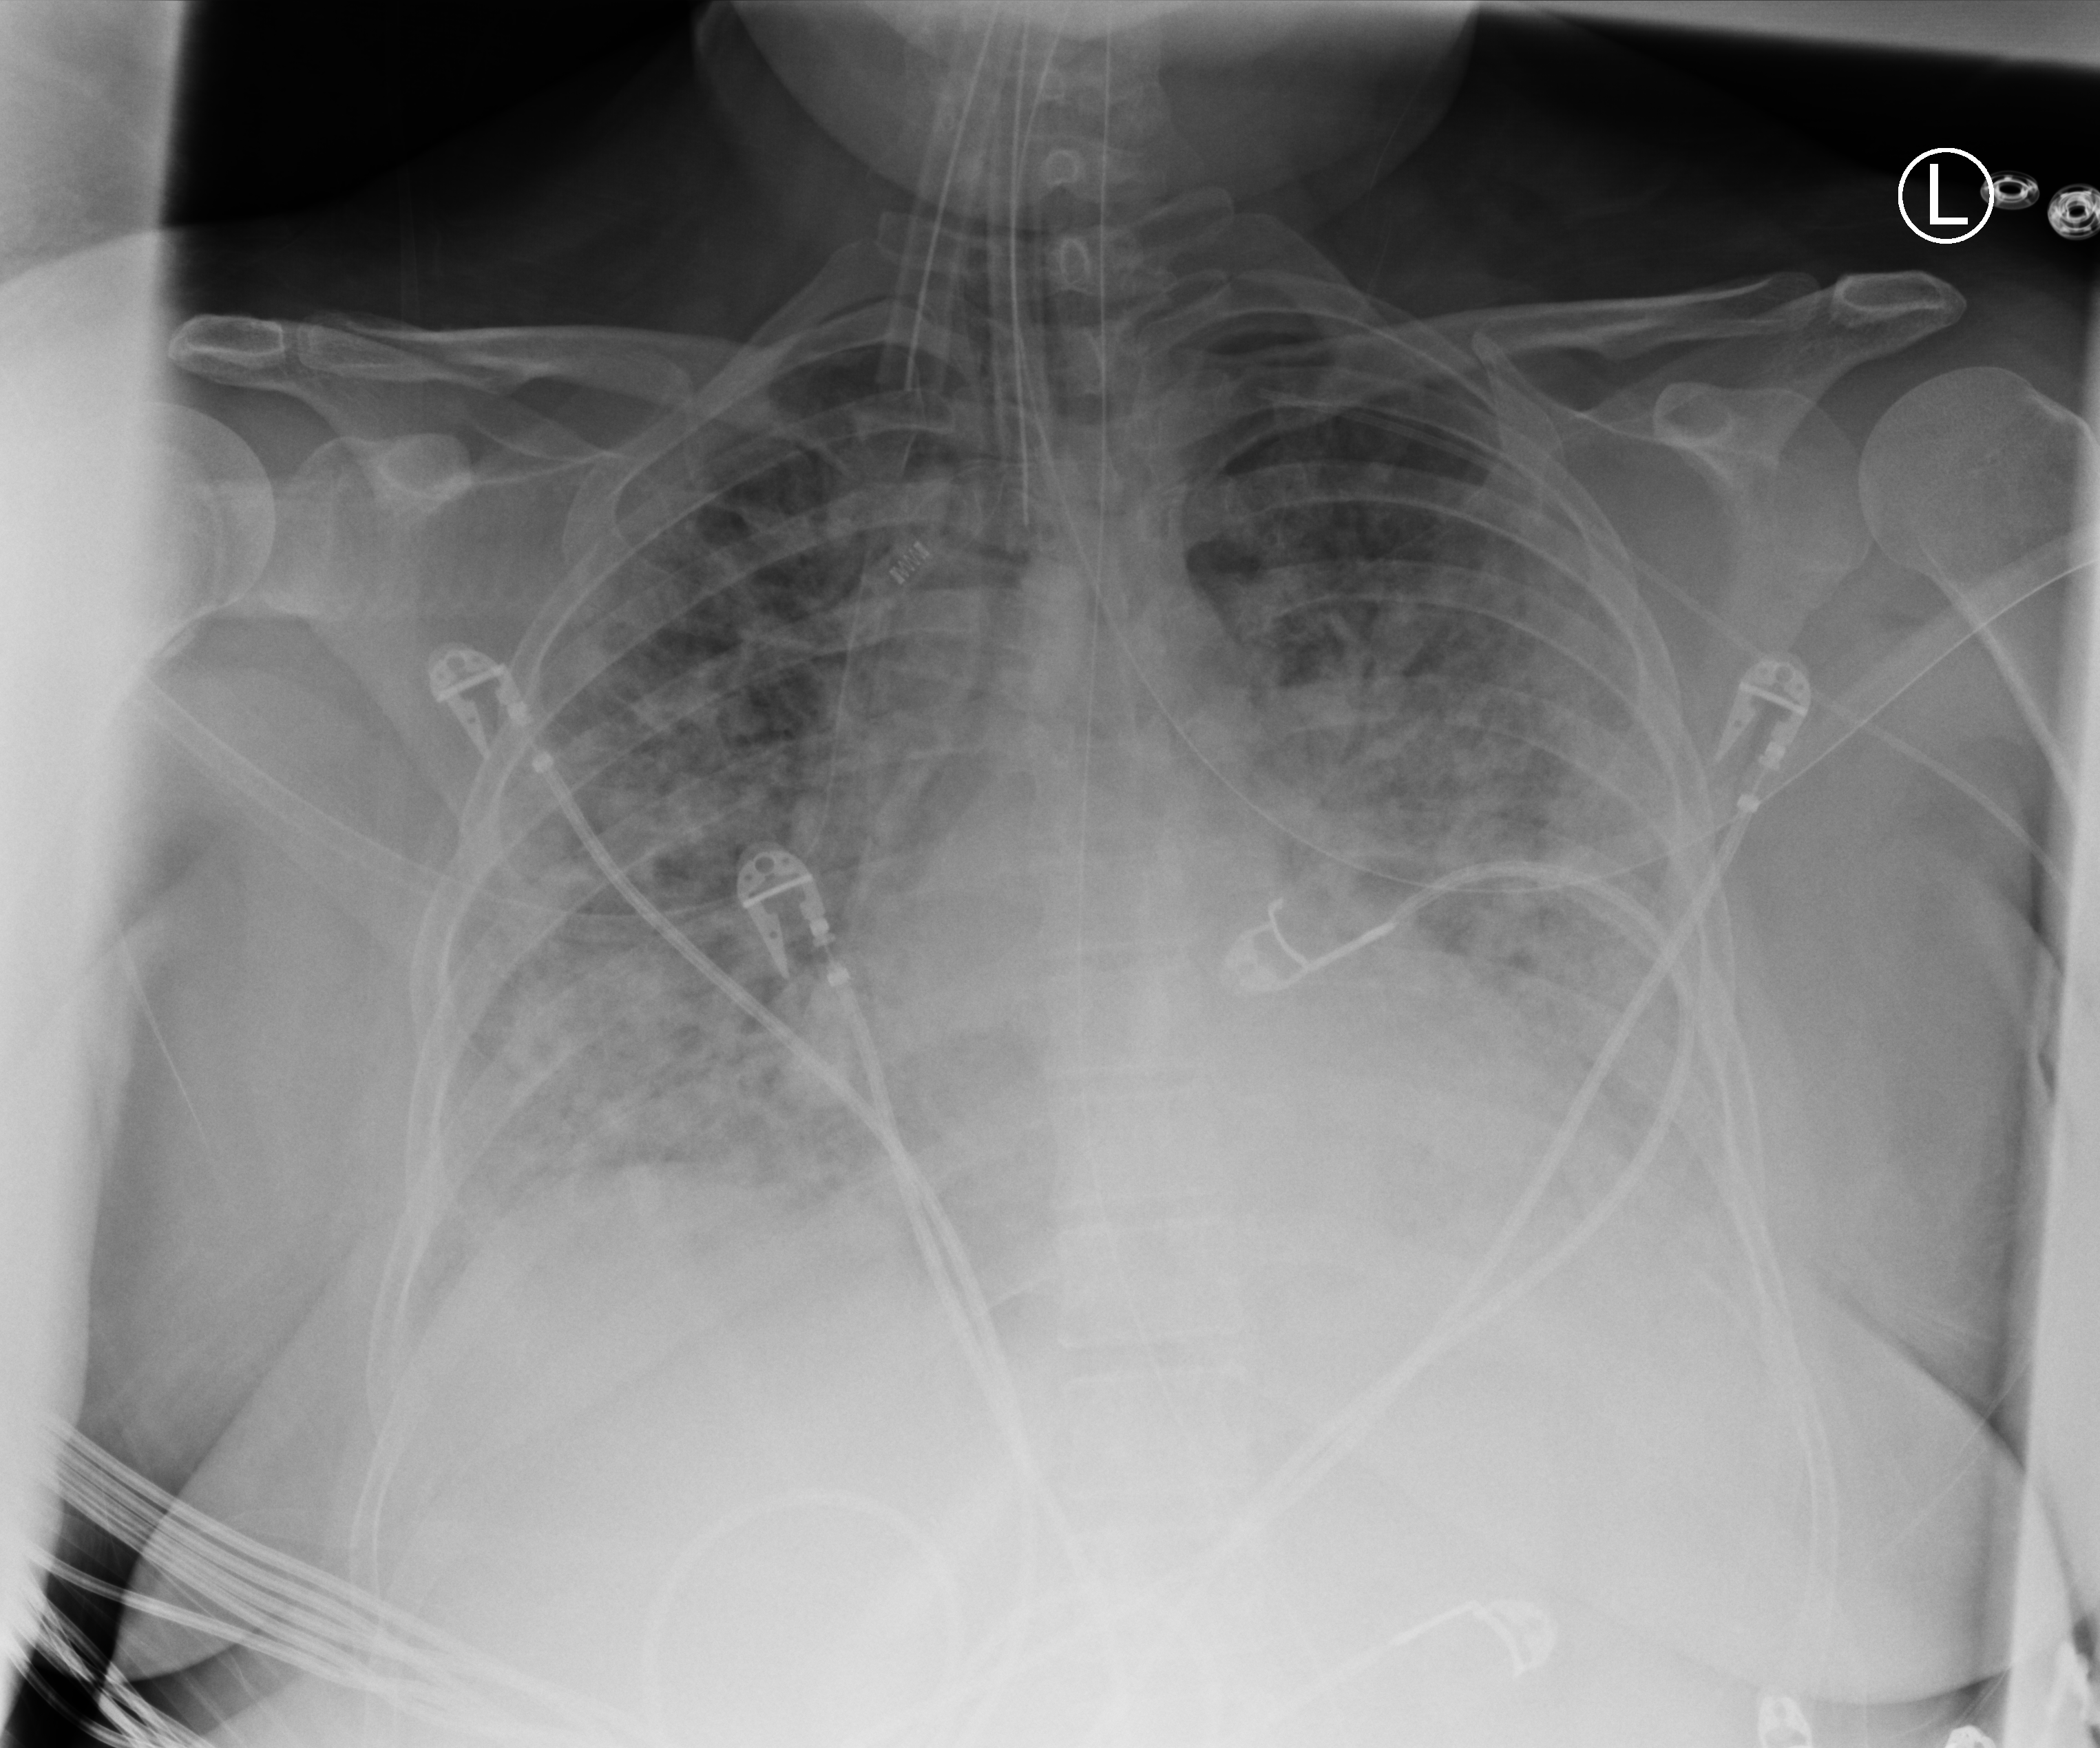
Chest X-ray (portable). Patient hospitalised with COVID-19; female, aged 18–59 years.
From the hospital-stay record, not from the radiograph (when in the stay this image was taken is not recorded):
- hypertension (admission record): yes